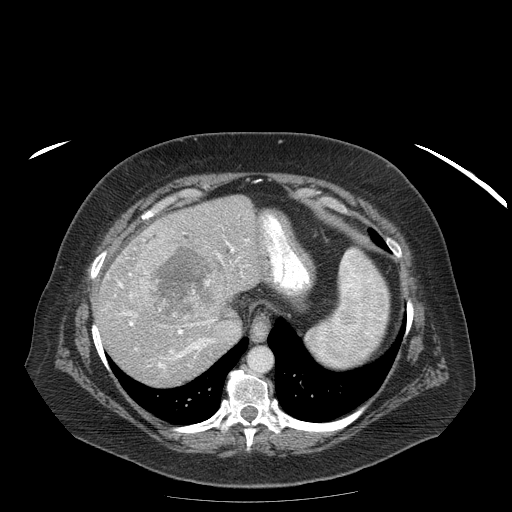
Contrast-enhanced abdominal CT (liver protocol), one axial slice; position 145 of 204 along the scan axis; reconstruction kernel STANDARD; soft-tissue window (W 400 / L 40 HU); 2.5 mm slice thickness; 512 × 512 image matrix, field of view 440 × 440 mm. Case-level facts recorded for this patient, not image findings: diagnosis: hepatocellular carcinoma (patient treated with transarterial chemoembolisation; whether this scan precedes or follows treatment is not stated here); TNM stage (as recorded): Stage-IIIB; Child-Pugh class: A; tumour differentiation: well differentiated.
Annotated regions visible in this slice (semi-automatically segmented with operator editing):
- liver parenchyma outside the tumour (the mass and vessels are separate outlines, so this box may not span the whole liver): box from (x=94, y=195) to (x=270, y=386) px
- mass: (x=137, y=234)–(x=224, y=328)
- liver vessels: (x=117, y=232)–(x=250, y=369)